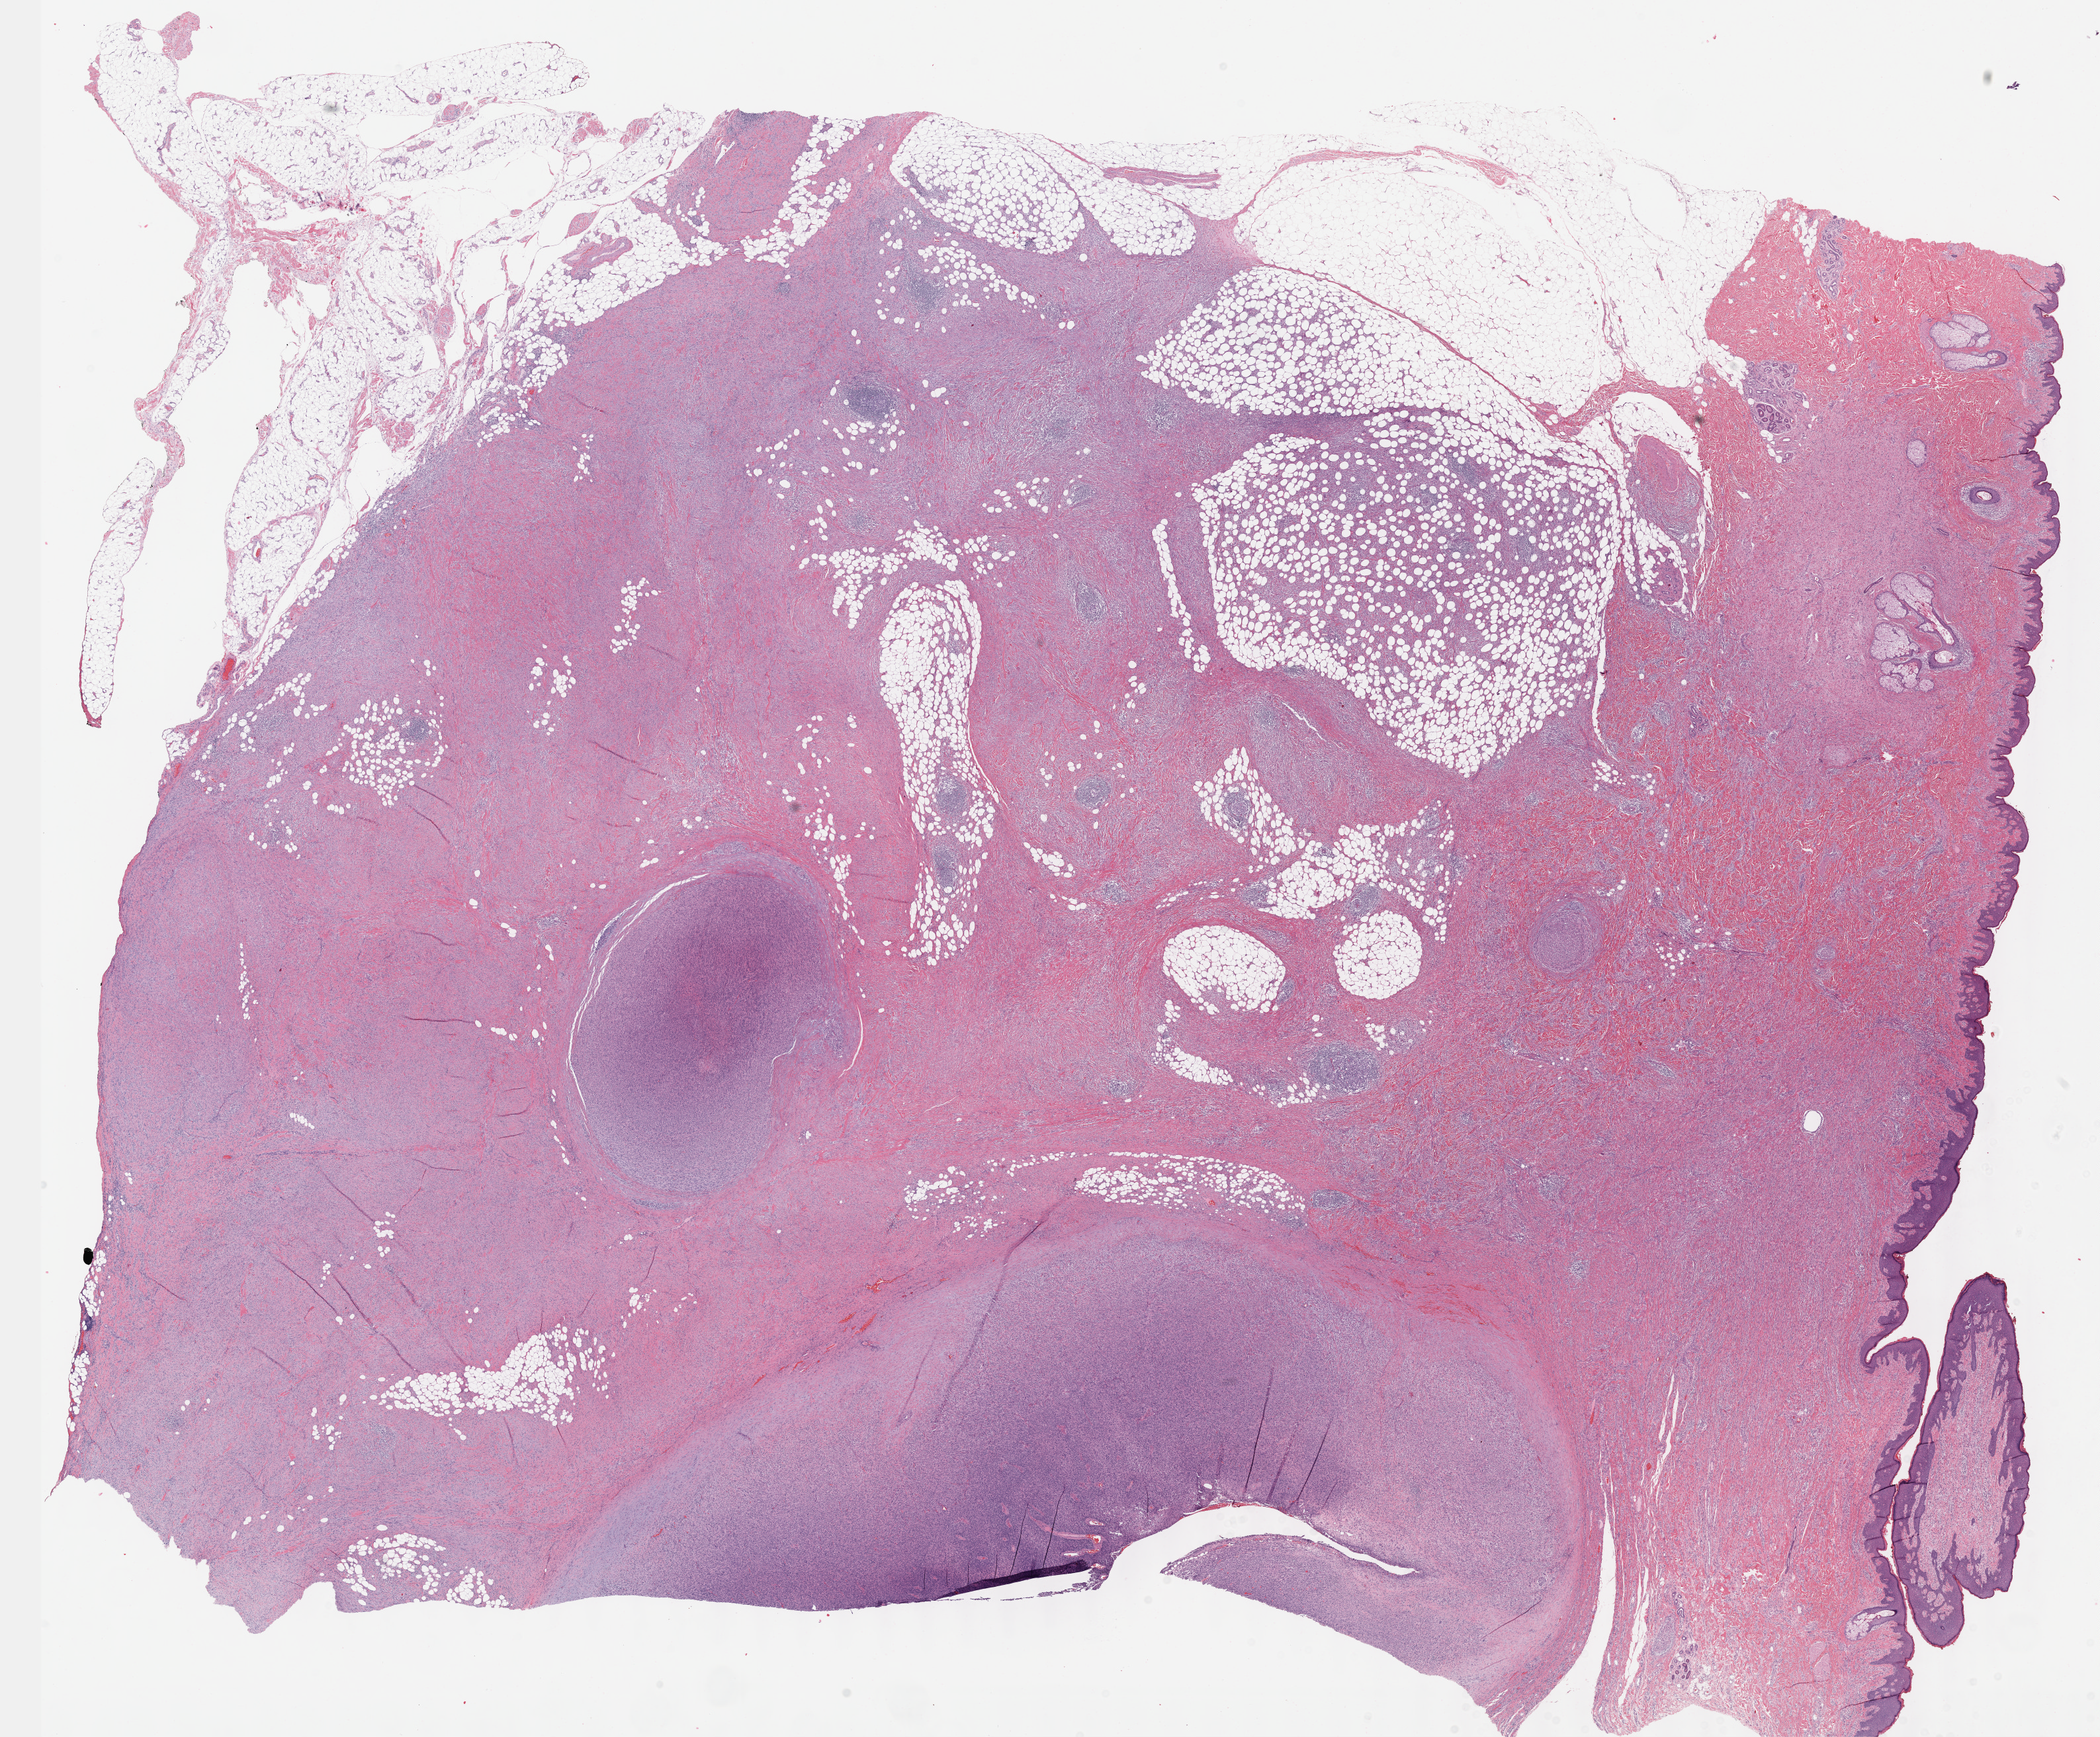
Whole-slide histology image, H&E — a low-resolution overview of the entire scanned area, about 25.7 x 21.2 mm (from a 40x scan). FFPE section. Sample: primary tumour, connective, subcutaneous and other soft tissues. Male patient; age at initial diagnosis 52 years.
Pathologic diagnosis: Malignant peripheral nerve sheath tumor (connective, subcutaneous and other soft tissues of trunk, NOS).